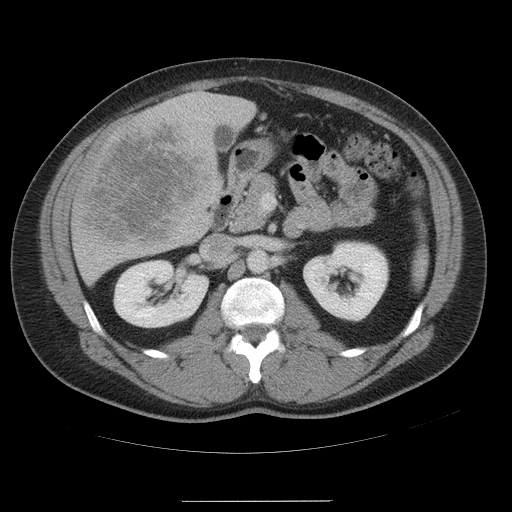
Contrast-enhanced abdominal CT, one axial slice; position 24 of 54 along the scan axis; 120 kVp; intravenous contrast given; soft-tissue window (W 400 / L 40 HU); 5 mm slice thickness; 512 × 512 image matrix. Male patient, age 40 years. From the clinical record (not read from this slice): diagnosis: colorectal cancer liver metastases, imaged before liver resection; multiple liver metastases: no; largest metastasis: 15 cm.
Outlined on this slice (outlined manually by an expert reader):
- liver: box from (x=71, y=92) to (x=255, y=285) px
- planned liver remnant (the part of the liver to remain after resection): (x=226, y=97)–(x=255, y=129)
- liver metastasis: (x=77, y=112)–(x=216, y=249)